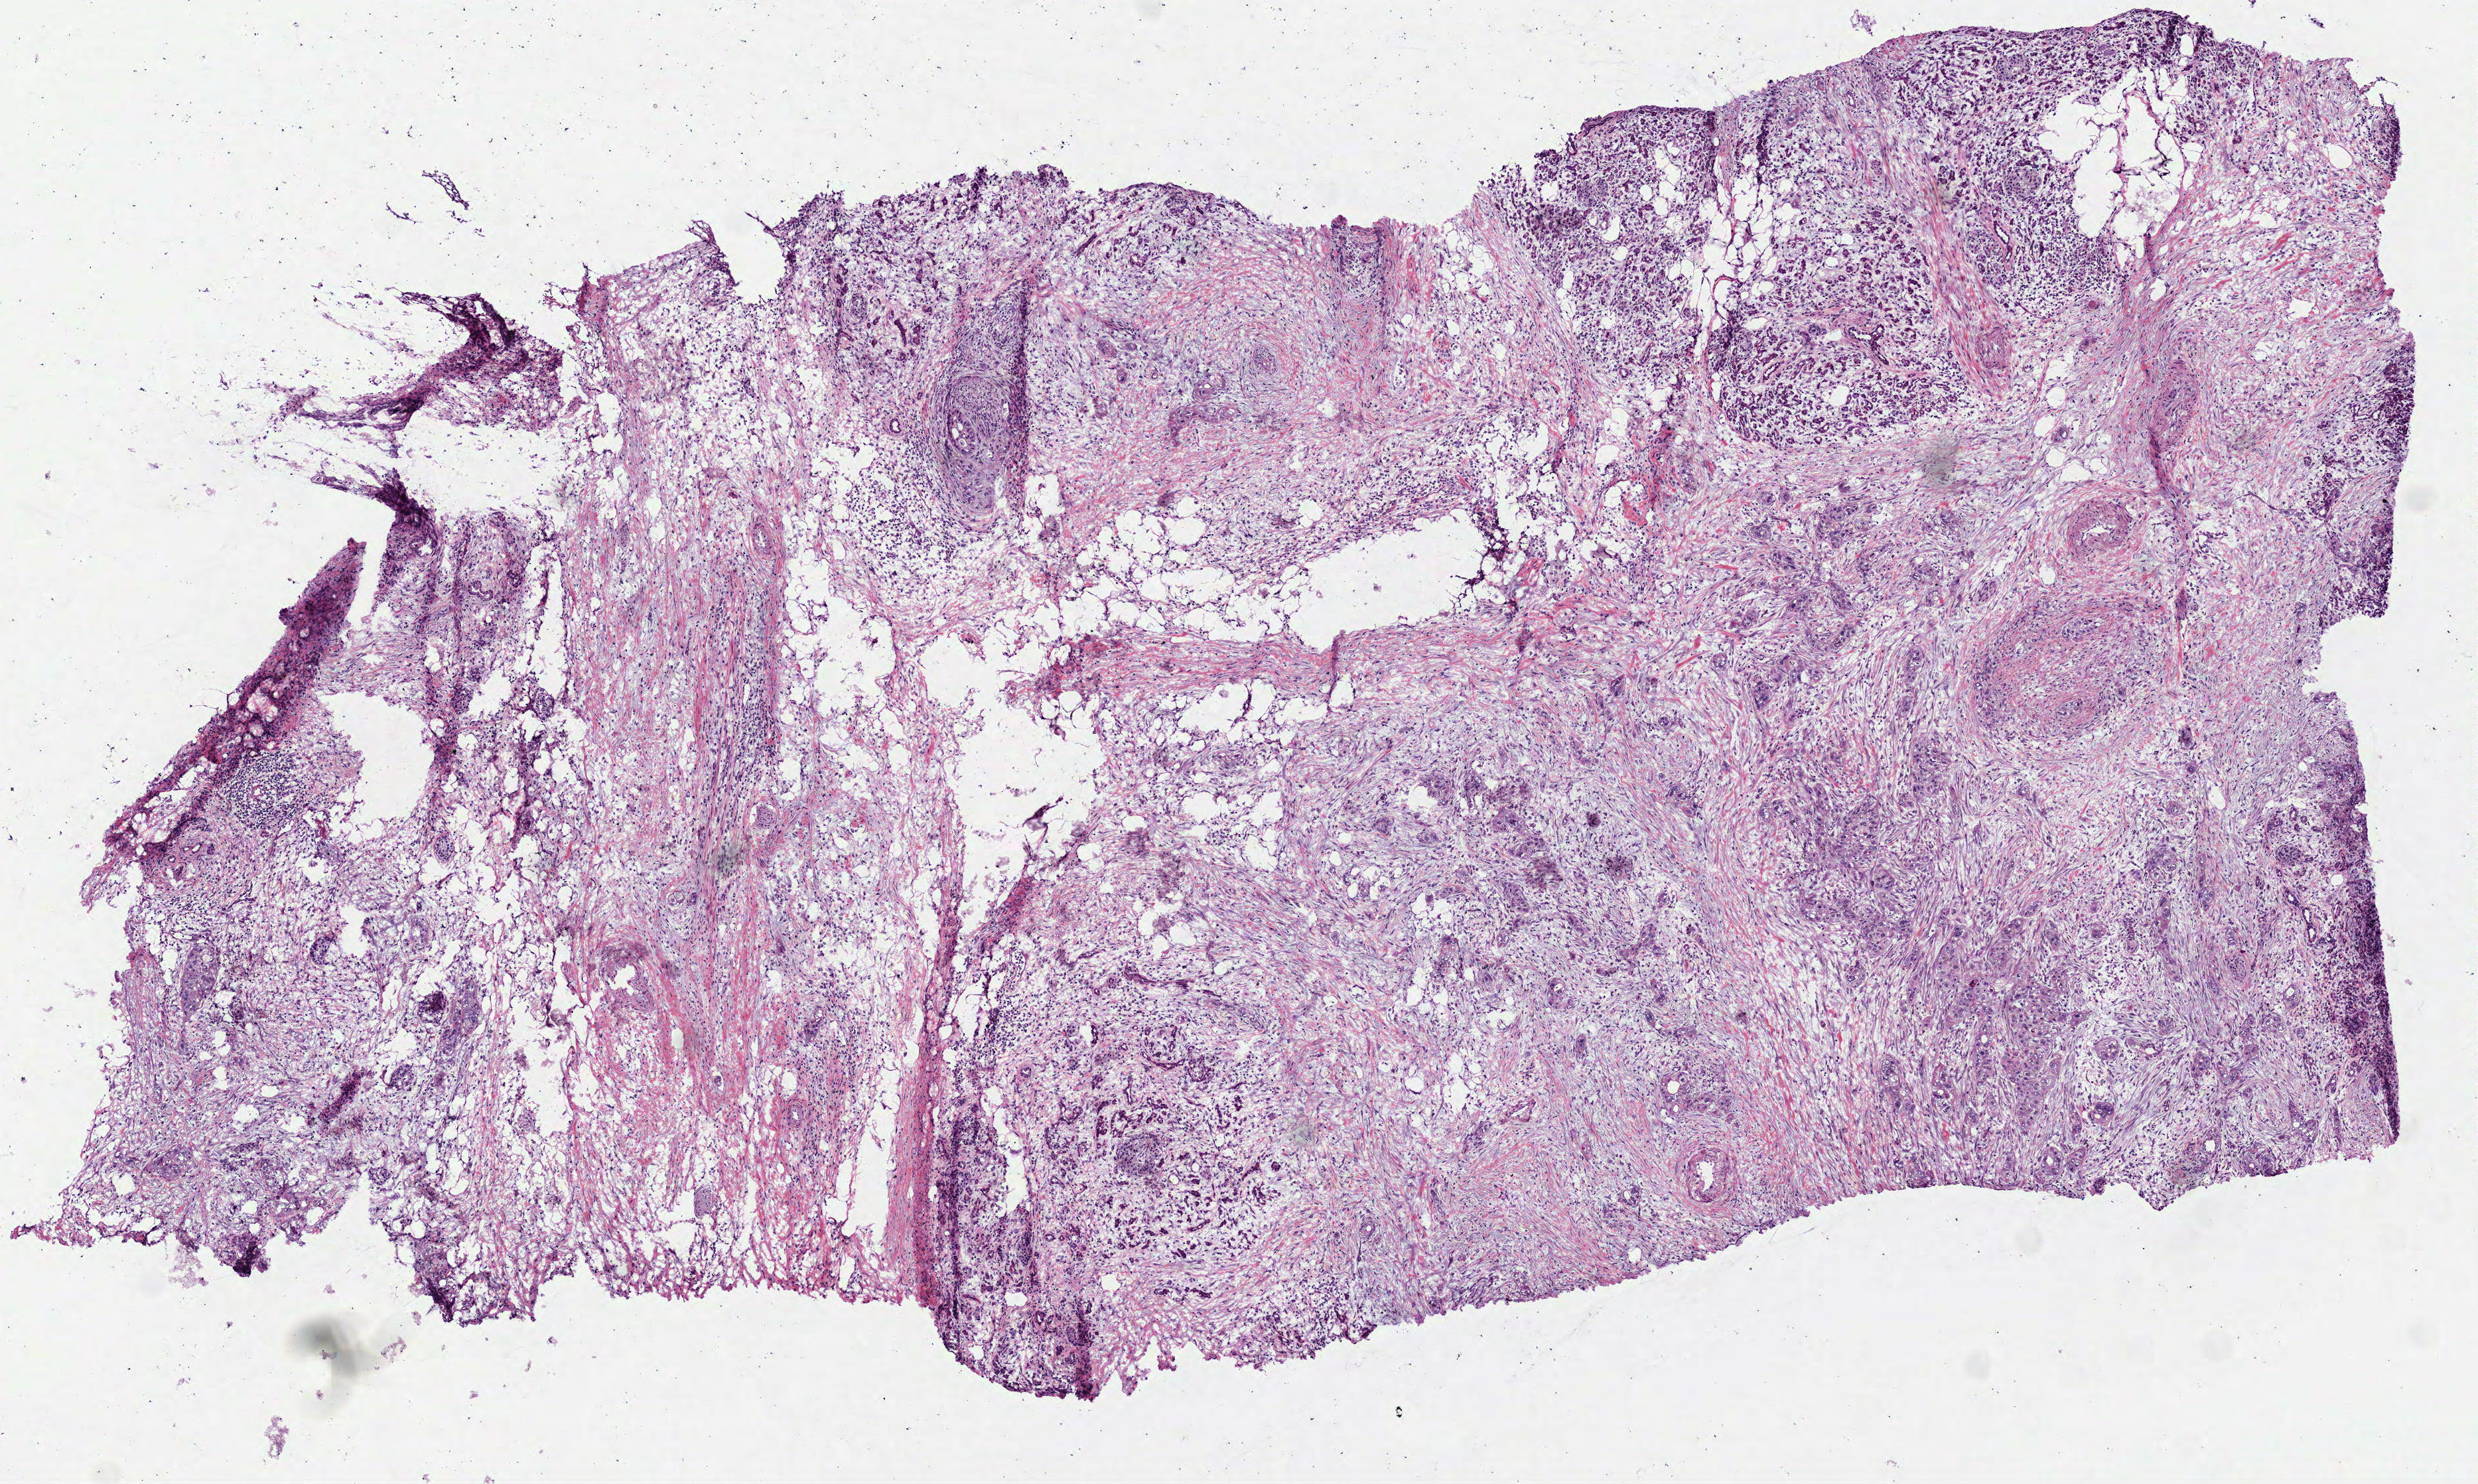
Hematoxylin and eosin (H&E) stained whole-slide image, a low-resolution overview of the entire scanned area, about 7.5 x 4.5 mm (slide scanned at 40x), frozen section from the bottom of the tissue portion, primary tumour sample from the pancreas. Male patient; age at initial diagnosis 61 years. Histologic grade: G2 (moderately differentiated).
Diagnosis: Infiltrating duct carcinoma, NOS (head of pancreas). AJCC pathologic stage: IIB (7th edition). TNM: T3 N1 MX.